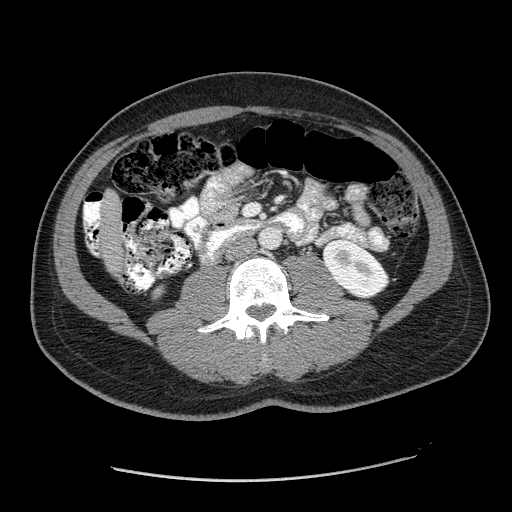
Contrast-enhanced abdominal CT (liver protocol), one axial slice. Position 29 of 182 along the scan axis. Reconstruction kernel STANDARD. Soft-tissue window (W 400 / L 40 HU). 2.5 mm slice thickness. 512 × 512 image matrix, field of view 400 × 400 mm. From the clinical record (not read from this slice): diagnosis: hepatocellular carcinoma (patient treated with transarterial chemoembolisation; whether this scan precedes or follows treatment is not stated here); TNM stage (as recorded): Stage-I; Child-Pugh class: A; tumour nodularity: uninodular.
Outlined on this slice (semi-automatically segmented with operator editing):
- liver parenchyma outside the tumour (the mass and vessels are separate outlines, so this box may not span the whole liver): bounding box [x1, y1, x2, y2] px = [84, 191, 120, 270]
- liver vessels: [84, 203, 94, 224]